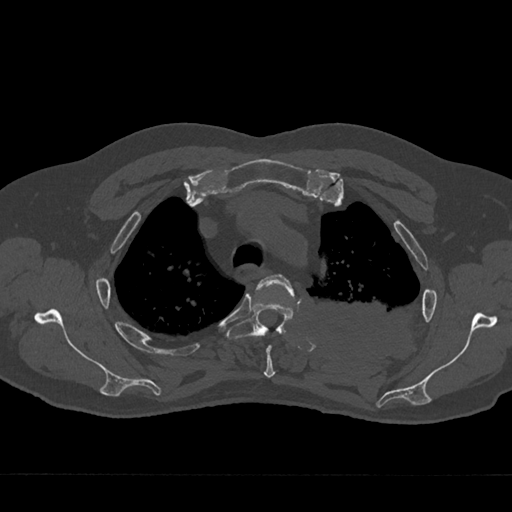
CT including the spine, one axial slice; position 538 of 797 along the scan axis; 120 kVp; bone window (W 1800 / L 400 HU); 0.5 mm slice thickness; 512 × 512 image matrix. Male patient, age 75 years. From the clinical record (not read from this slice): primary cancer: renal.
Structures marked on this image (semi-automatic segmentation, software-assisted and operator-edited):
- T3 vertebra: bounding box (x1, y1, x2, y2) in pixels: (256, 274, 294, 378)
- T4 vertebra: (227, 301, 294, 339)